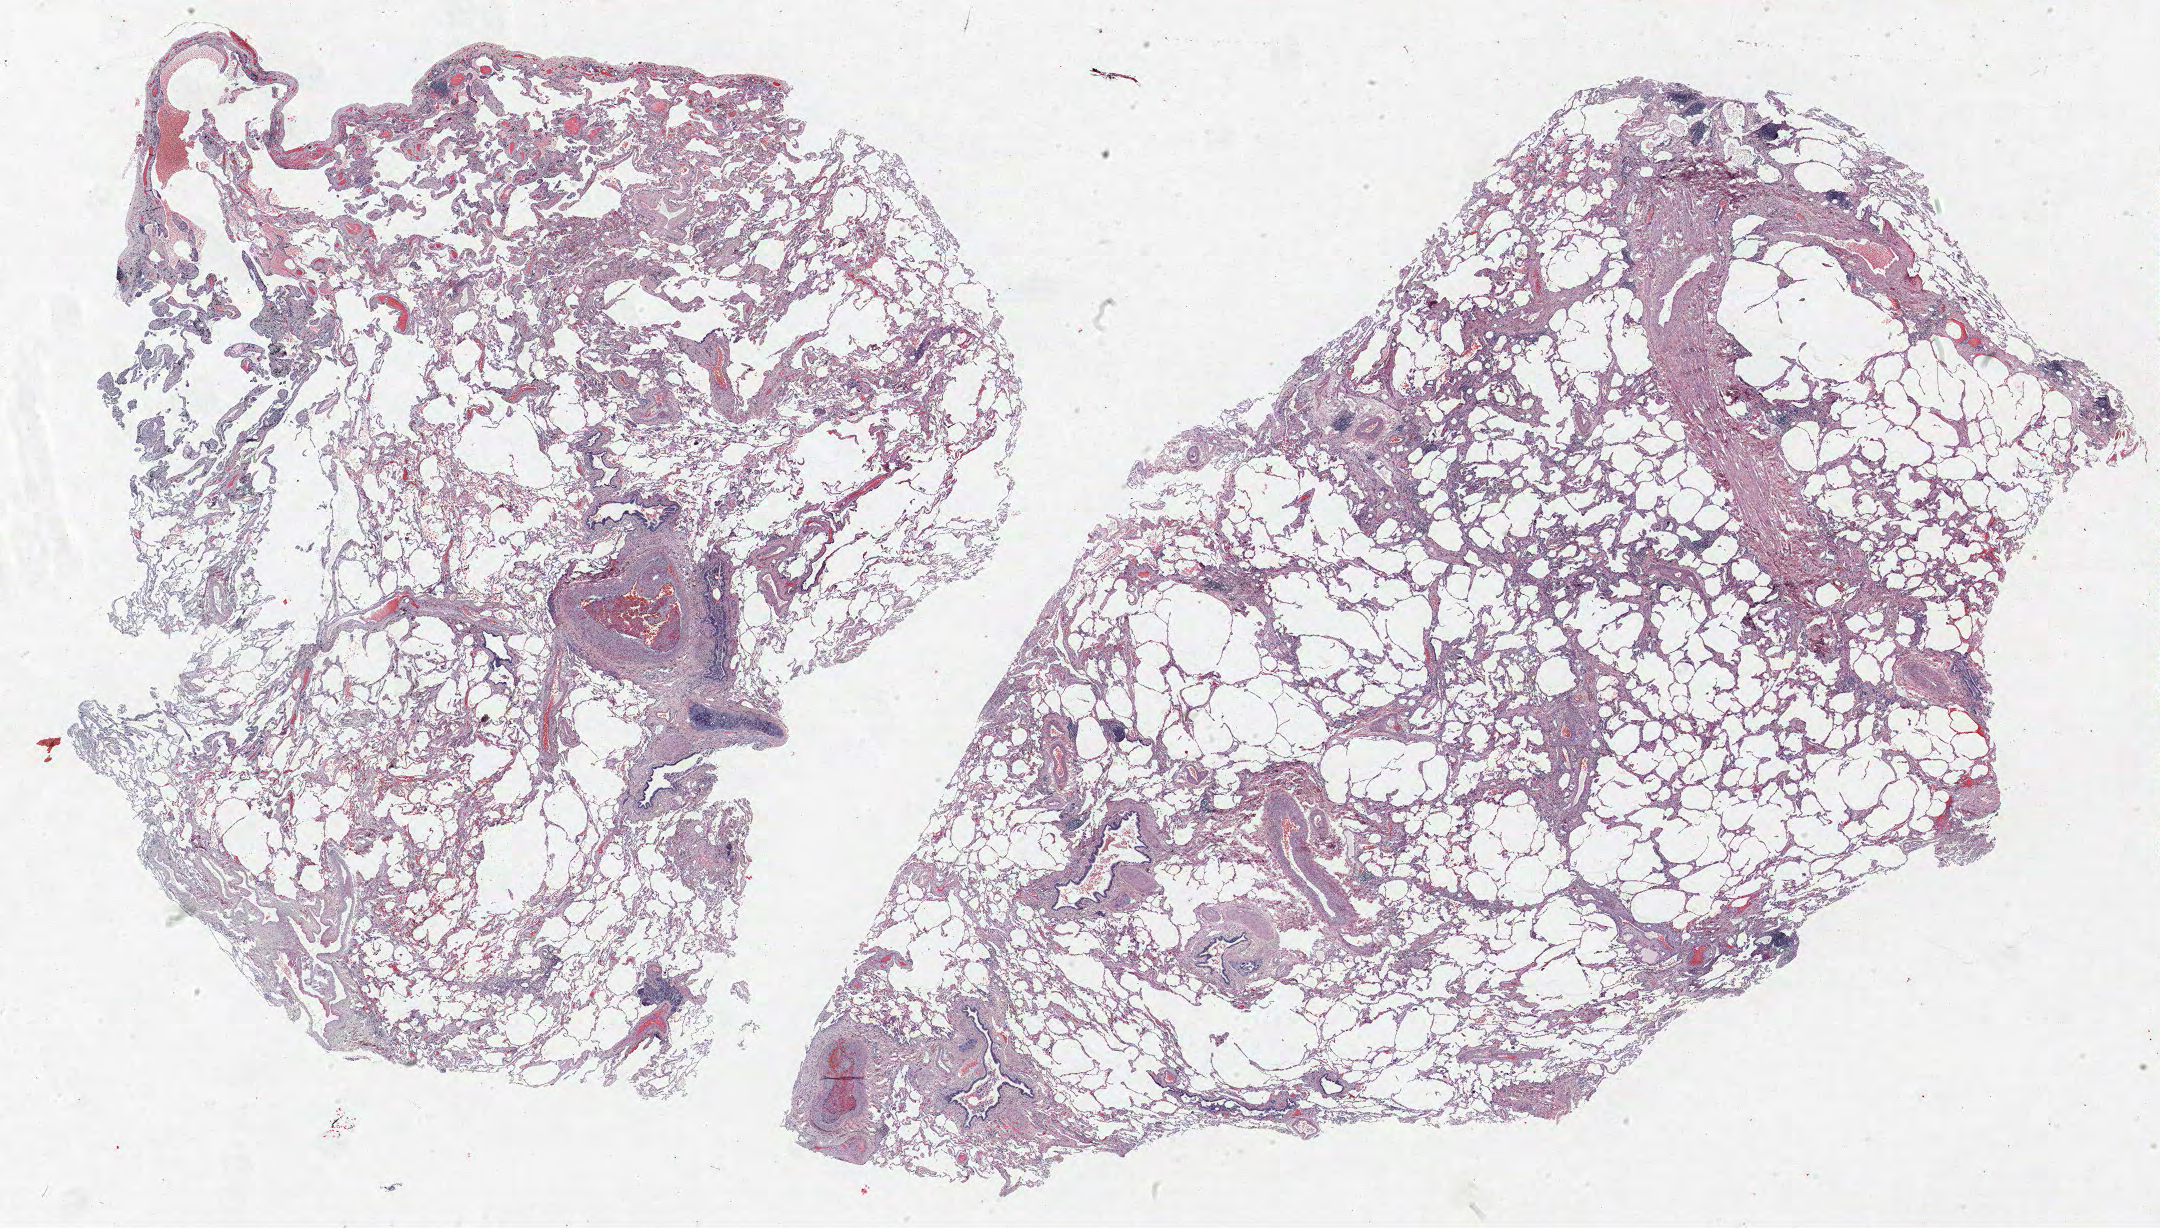
Whole-slide histology image, H&E, a low-resolution overview of the entire scanned area, about 34.6 x 19.7 mm (from a 40x scan). Formalin-fixed paraffin-embedded (FFPE) section. Lung. Male, age 68 at enrolment. Former smoker at enrolment.
Participant's lung-cancer diagnosis: Squamous cell carcinoma, NOS (ICD-O-3 8070/3).